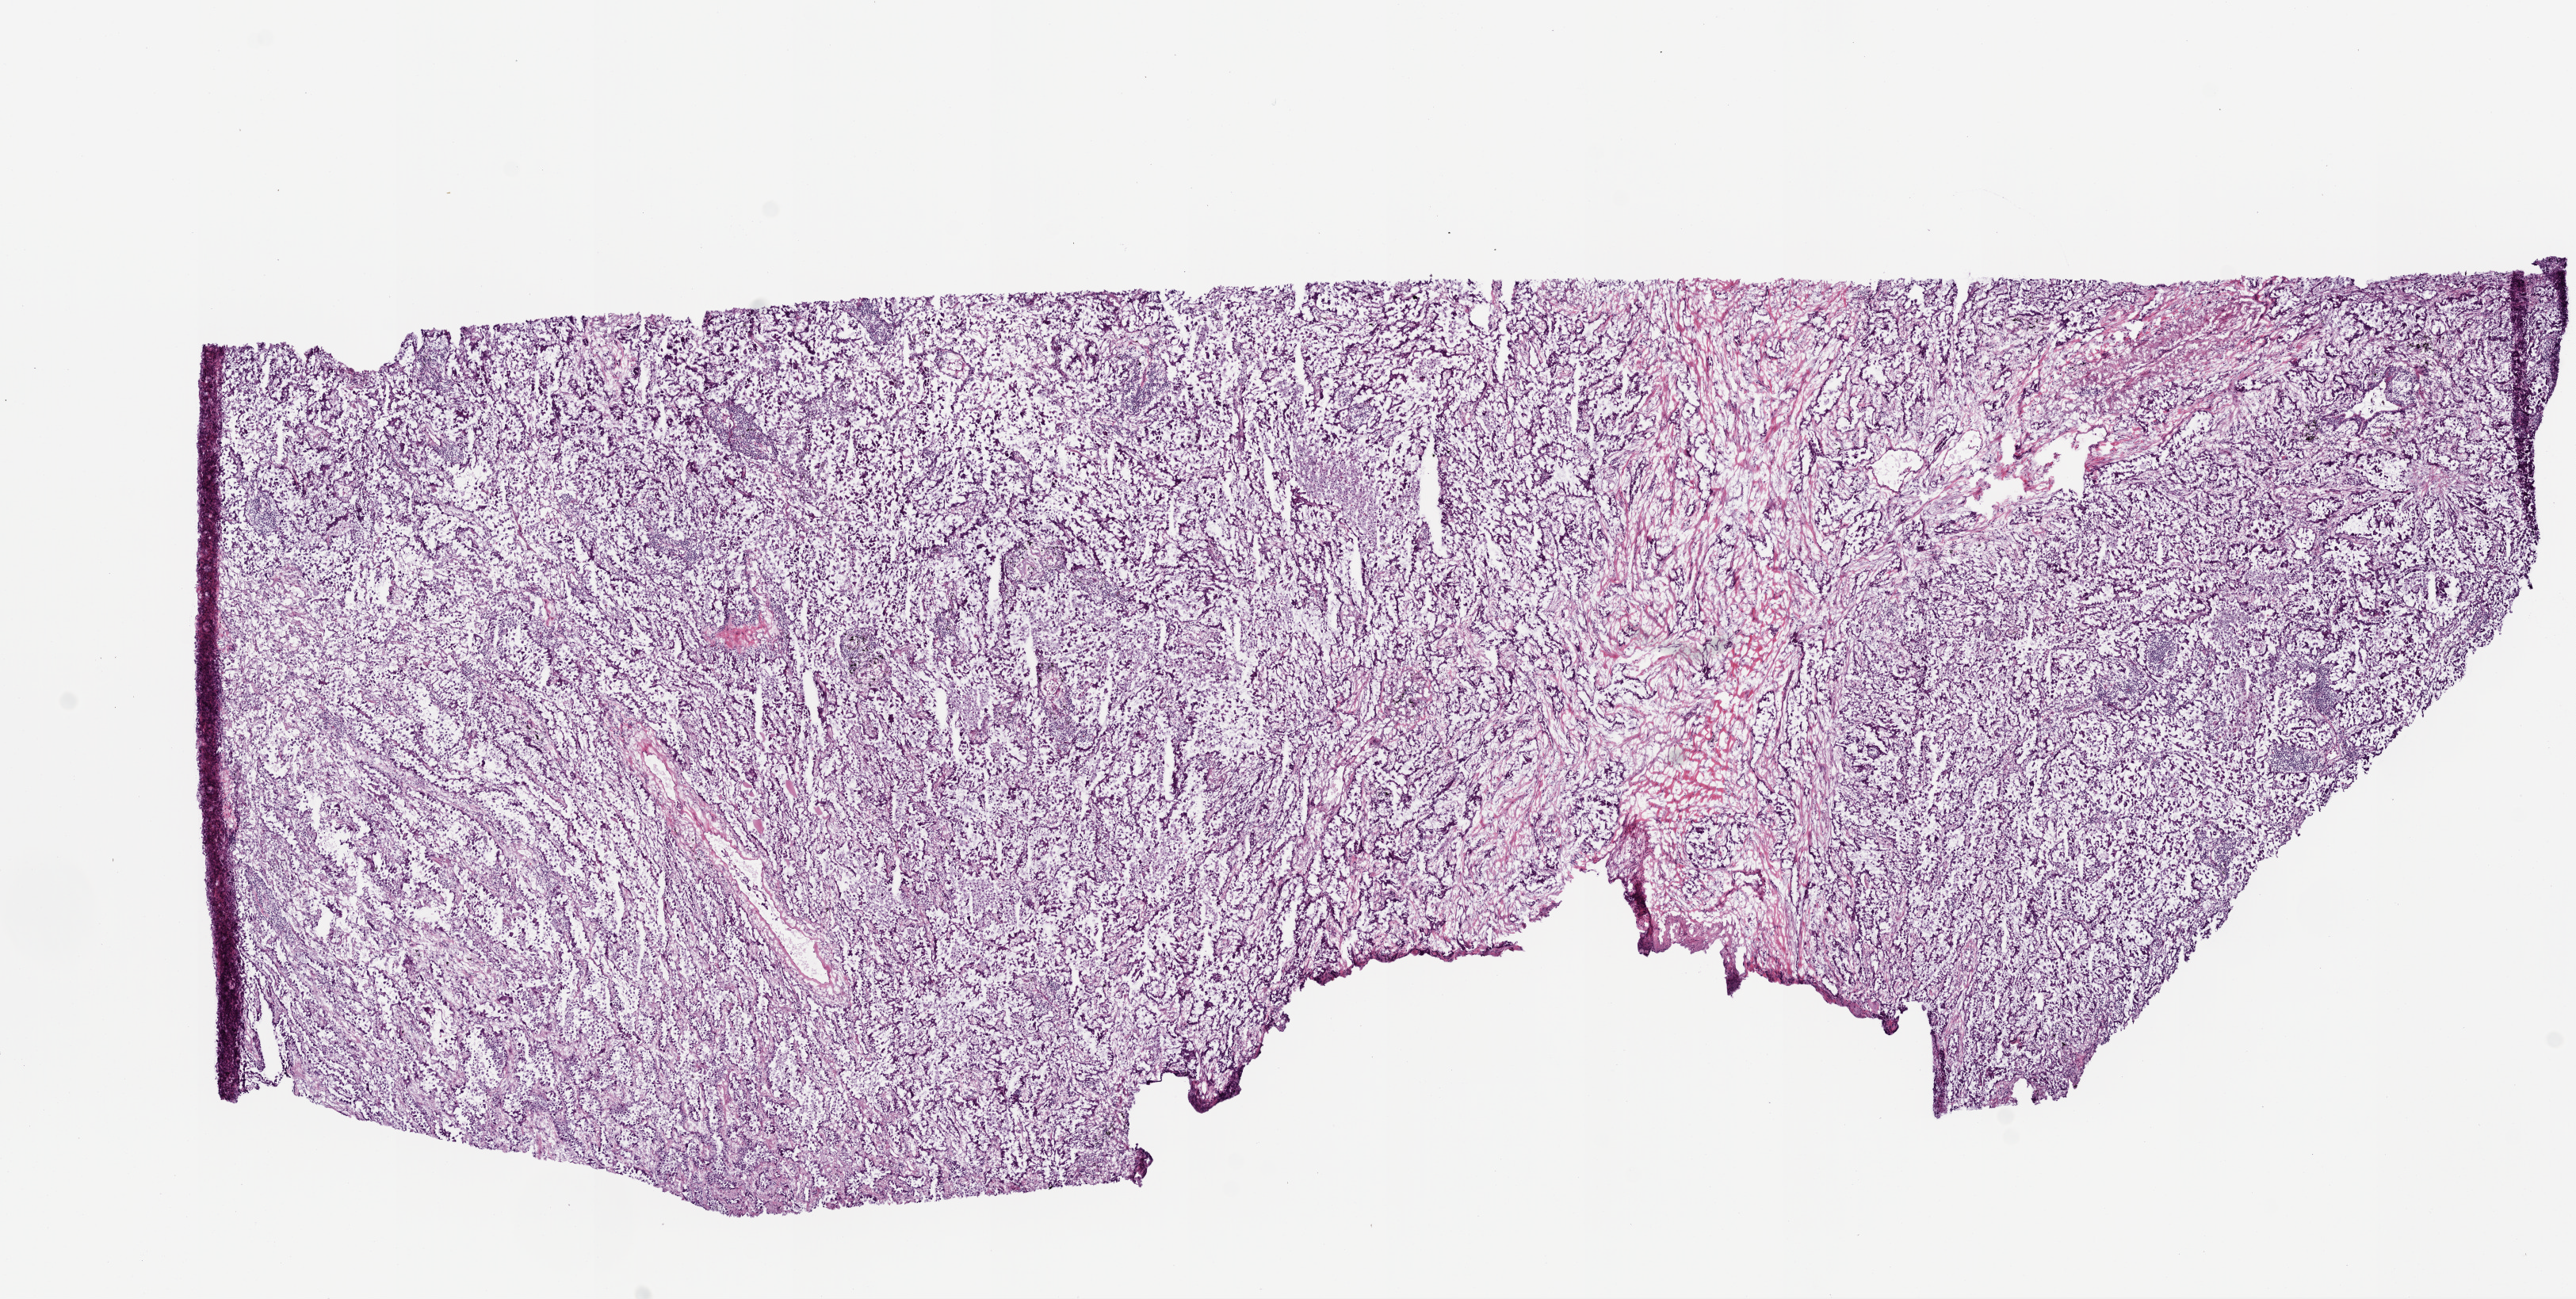
Hematoxylin and eosin (H&E) stained whole-slide image, whole scanned area (about 13.0 x 6.6 mm) shown as a low-resolution overview; frozen section; primary tumour sample from the lung. Male patient; age at initial diagnosis 65 years. Slide review estimates, as recorded: tumour cells 90%, tumour nuclei 70%, normal cells 0%, stromal cells 10%, necrosis 0%. Inflammatory infiltration, as recorded: lymphocyte infiltration 18%, monocyte infiltration 10%, neutrophil infiltration 0%.
TNM: T2 N1 M0. AJCC pathologic stage: IIB. Histologic diagnosis: Adenocarcinoma with mixed subtypes.